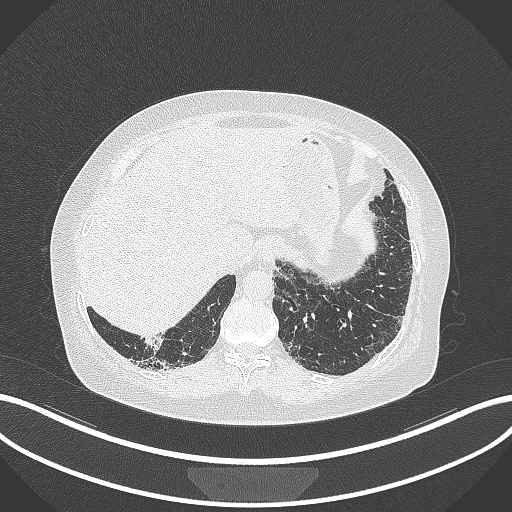
Chest CT, one axial slice. Slice 10 of 296 in the series (ordered by position). 120 kVp. Lung window (W 1500 / L -600 HU). 512 × 512 image matrix, field of view 400 × 400 mm. Female patient, age 65 years. From the clinical record (not read from this slice): clinical TNM (as recorded): T2b N1 M0; histopathological grade: G1.
Annotated regions visible in this slice (bounding box drawn by a radiologist):
- lung tumour (recorded histology: adenocarcinoma): bounding box [x1, y1, x2, y2] px = [140, 329, 167, 357]